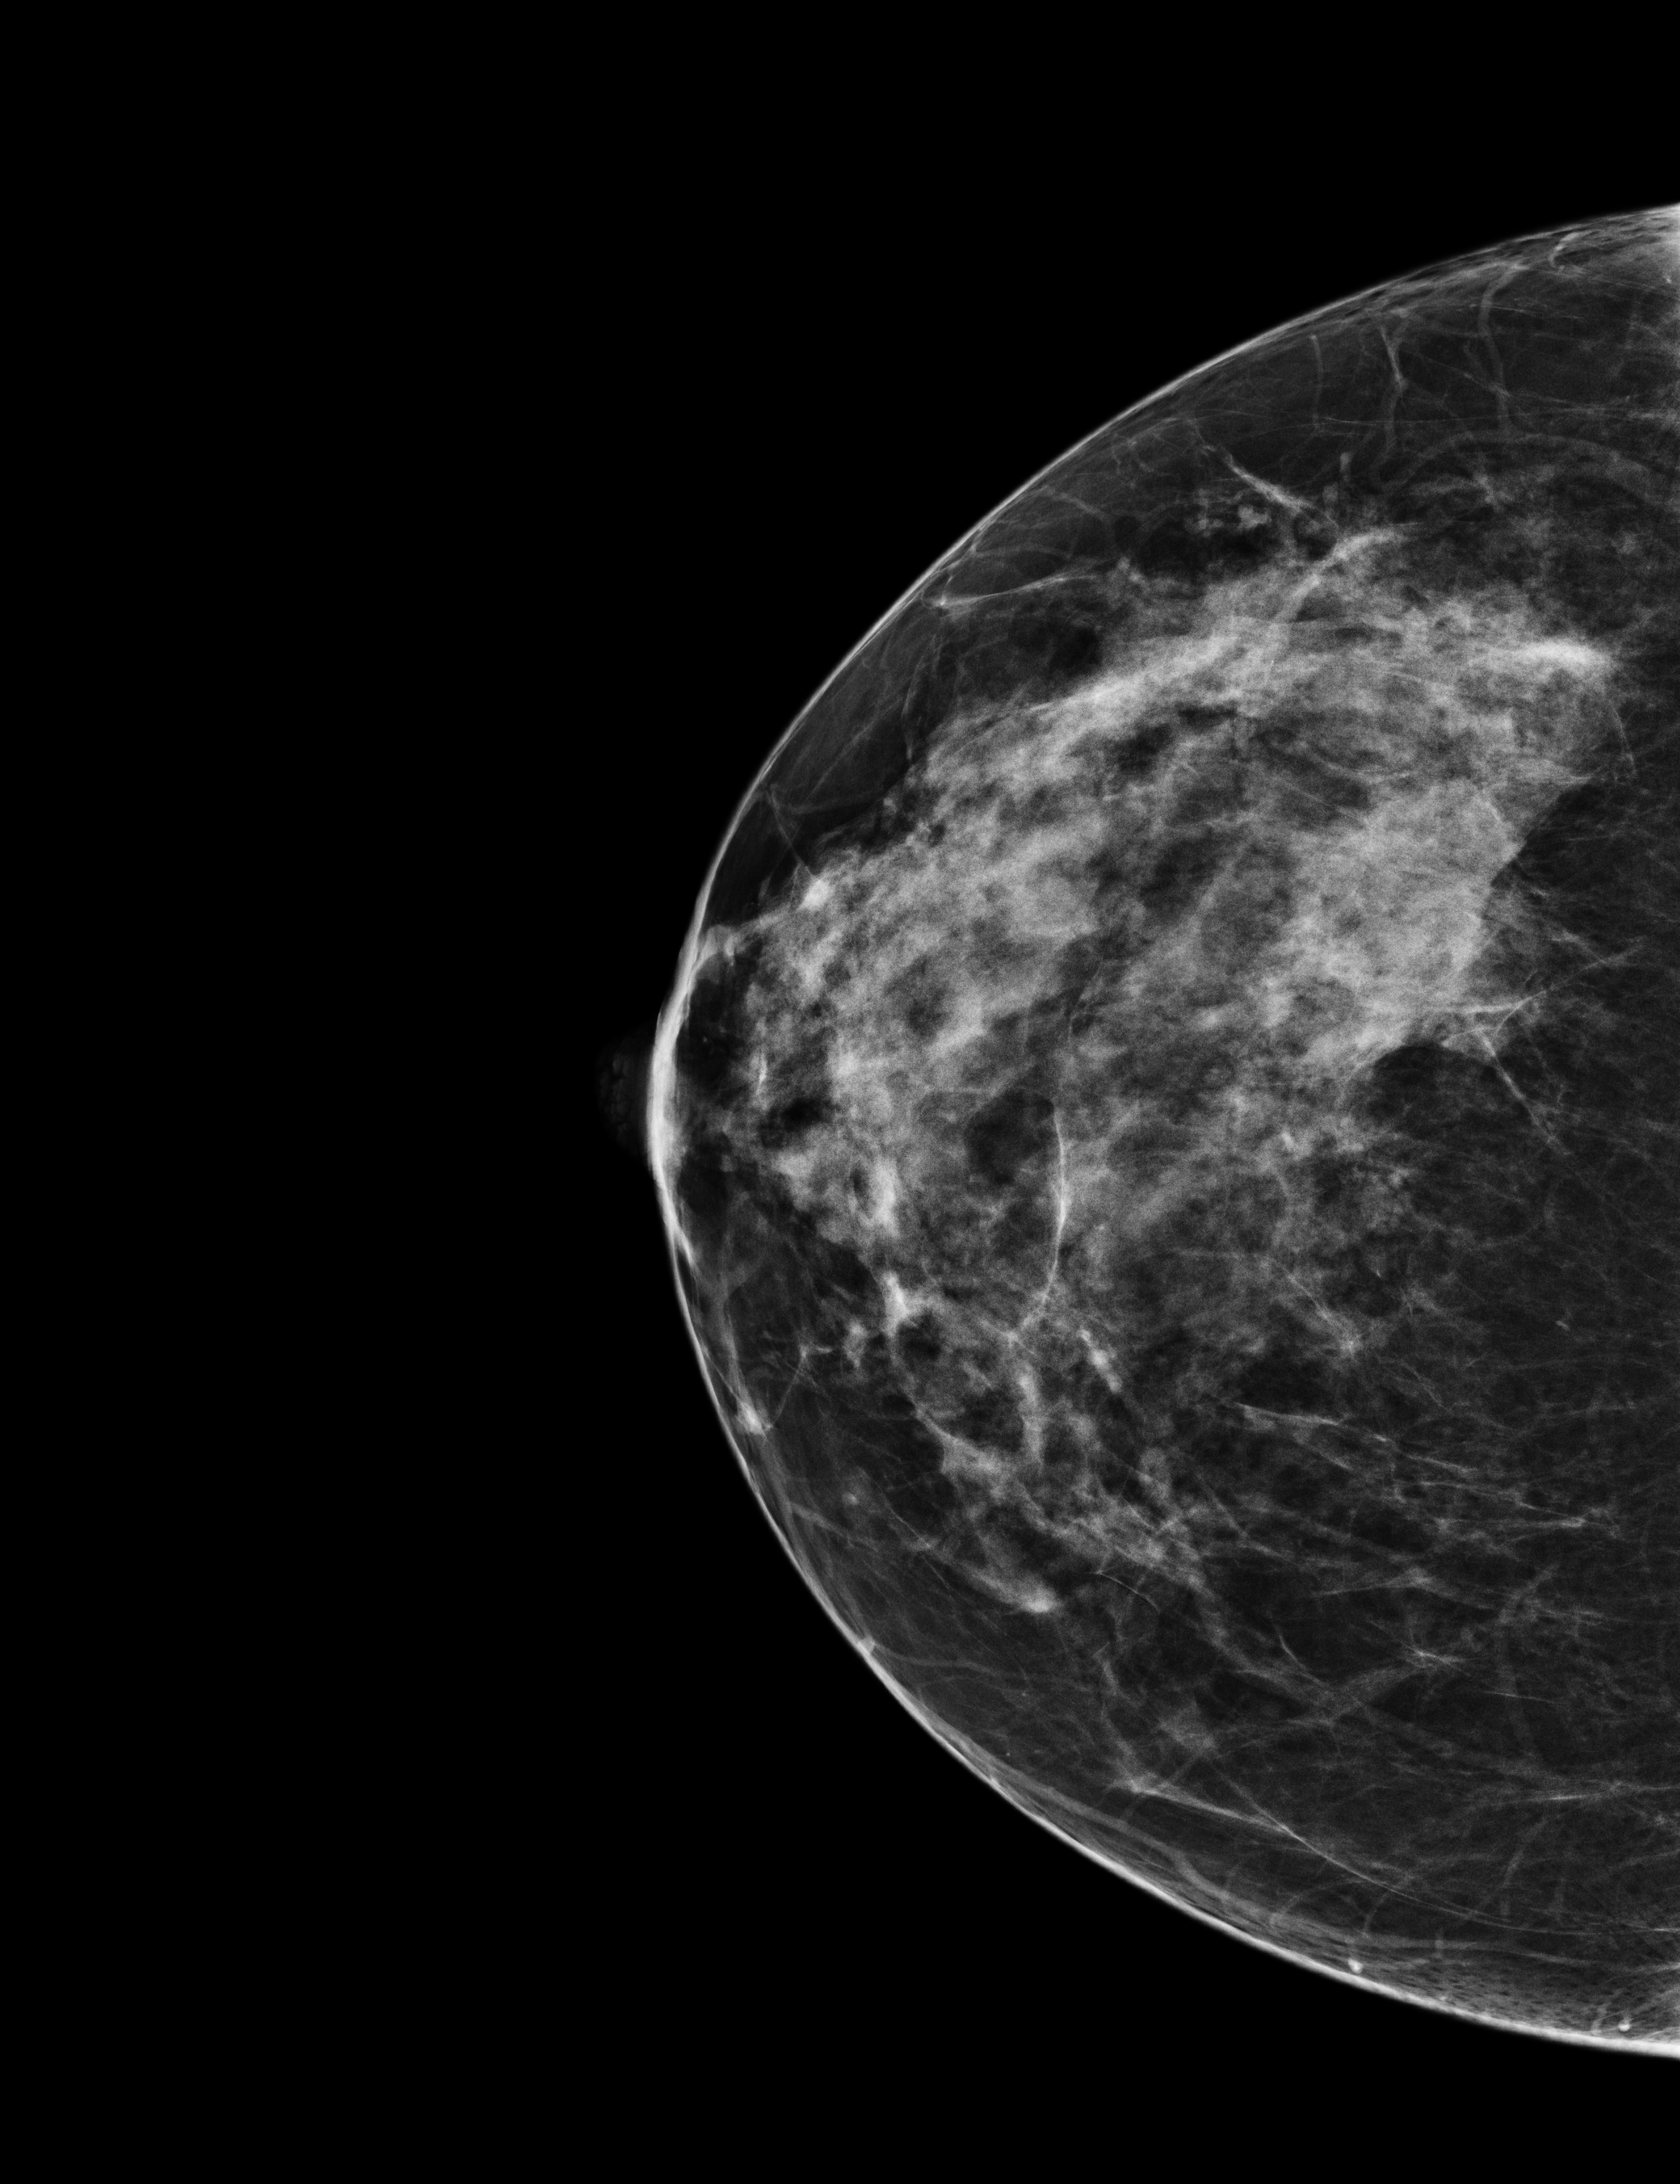
Screening examination, system: Selenia Dimensions. Patient: female, 42 years.
Image type: full-field digital mammogram. Breast: right. Projection: CC view.